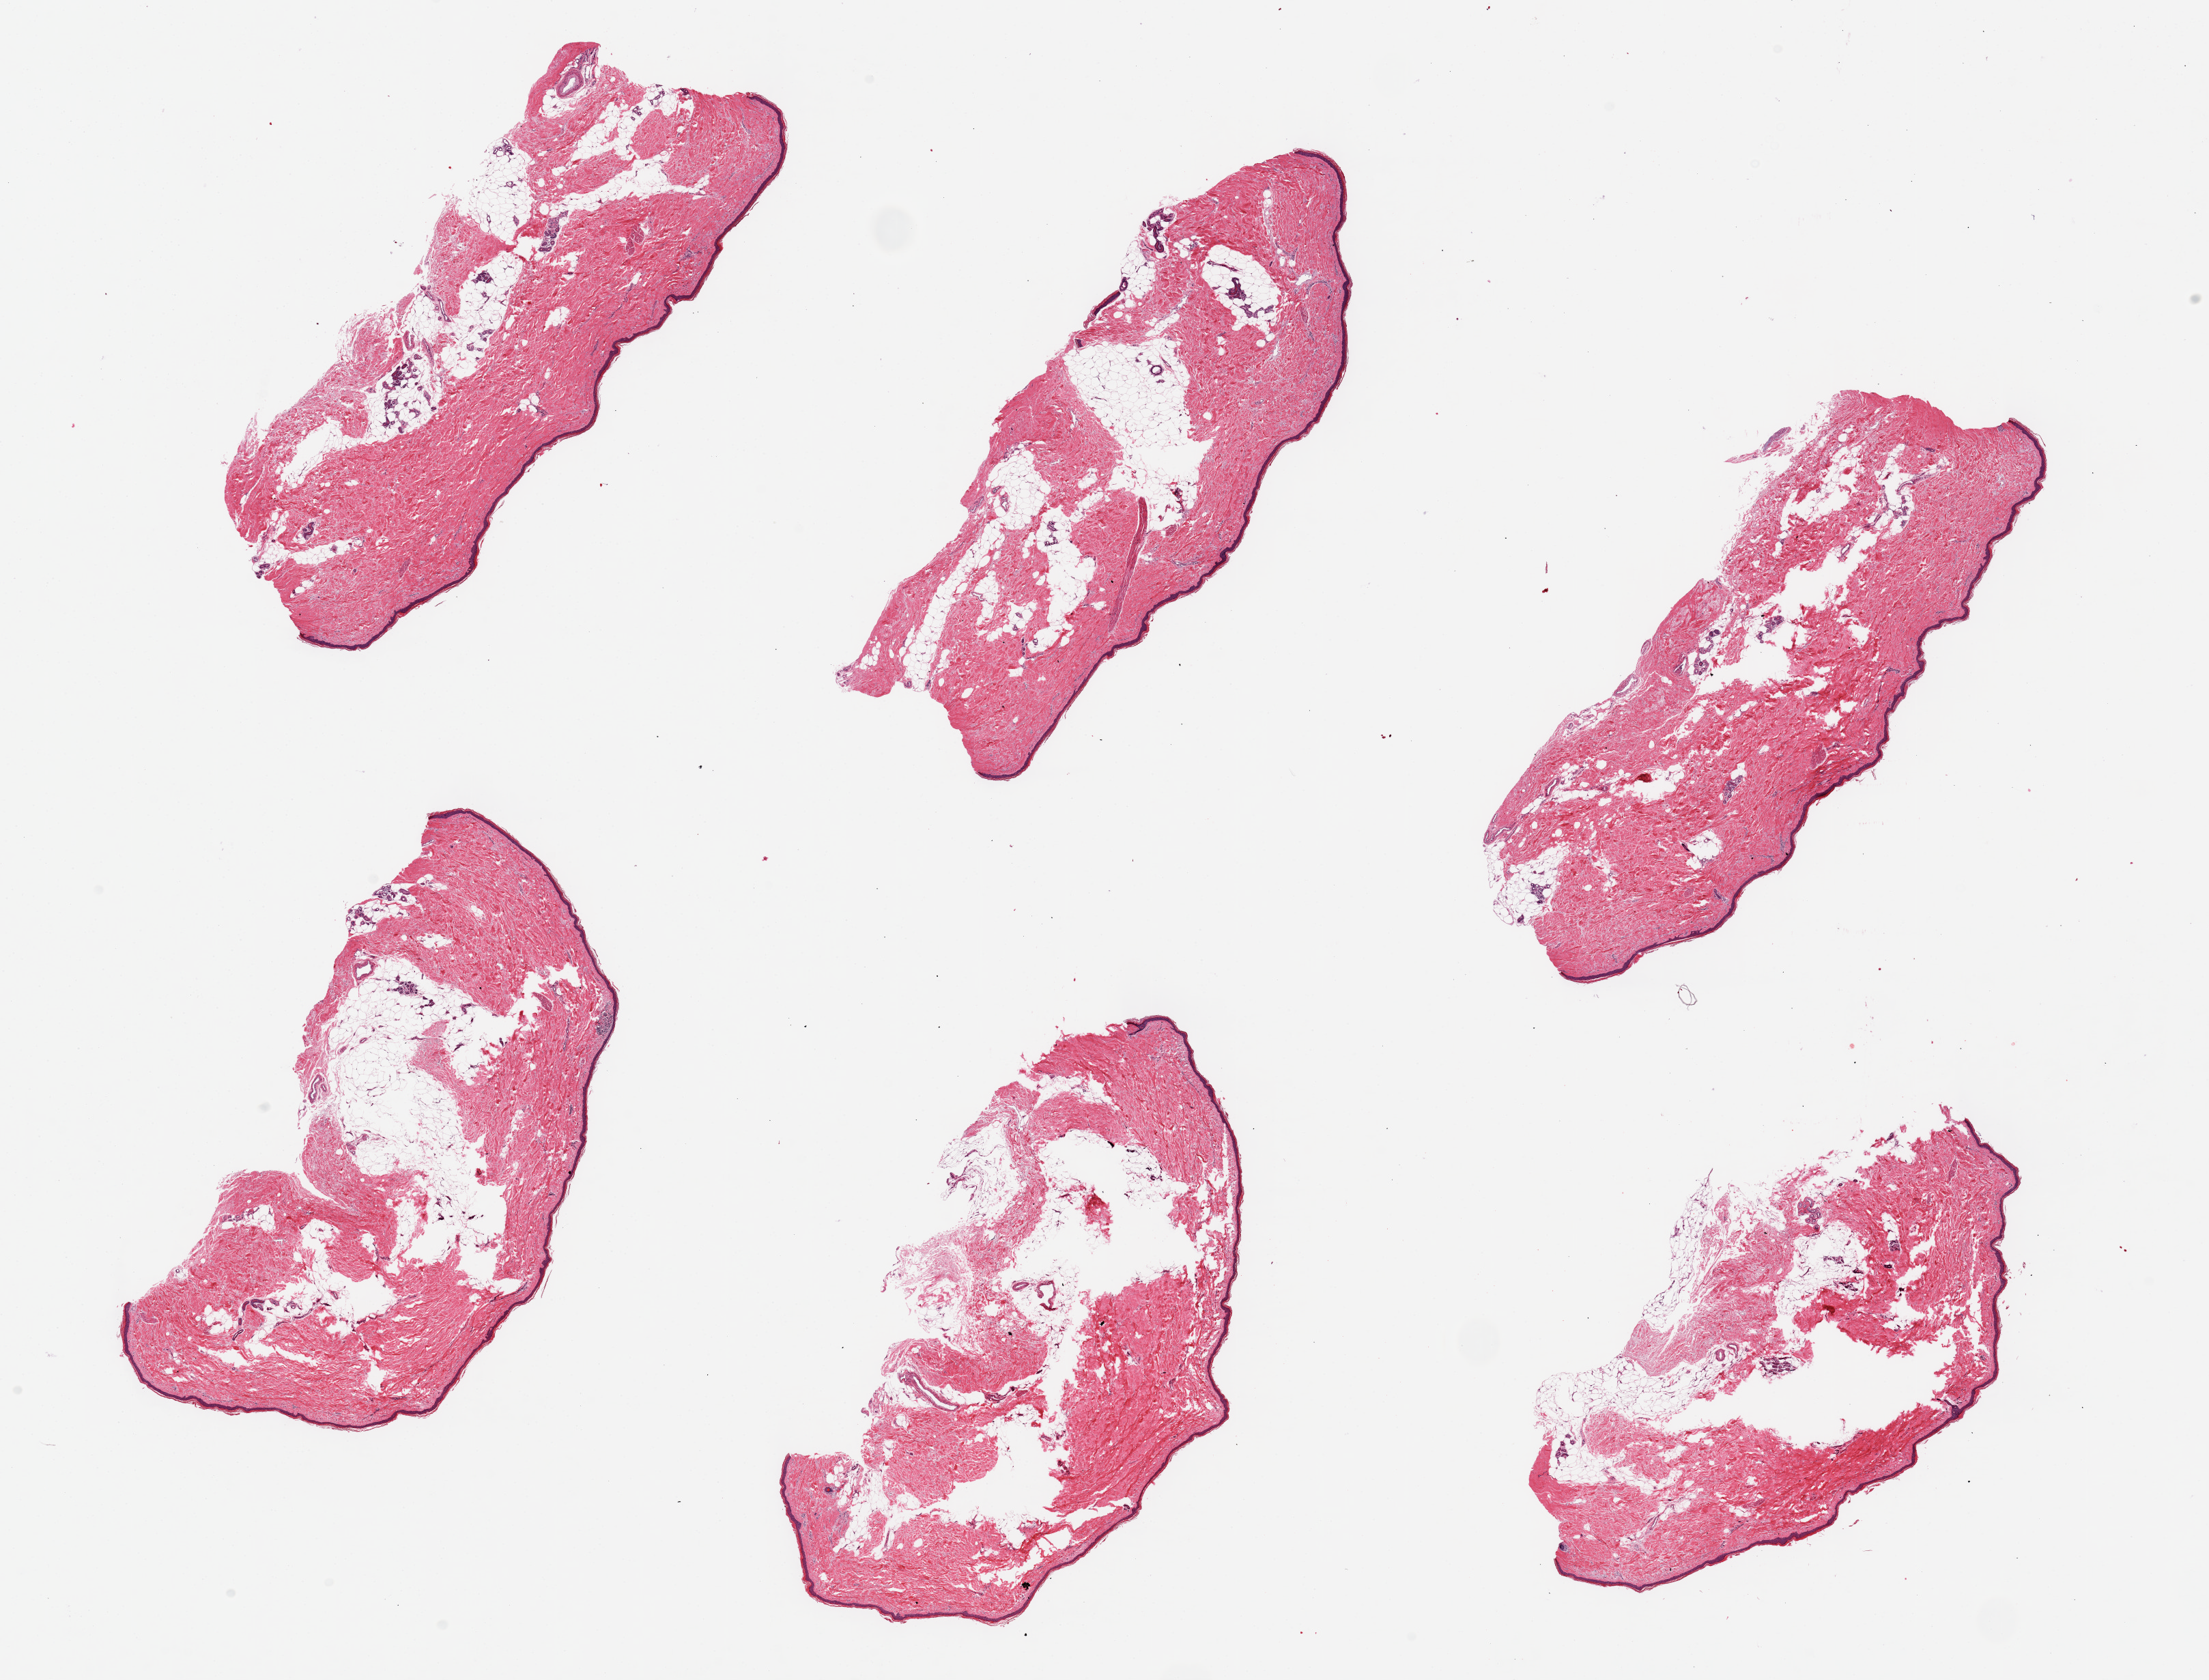
Whole-slide image, haematoxylin and eosin stain, low-resolution overview of the scanned area, about 25.6 x 19.5 mm (acquisition: 20x scan), PAXgene-fixed, paraffin-embedded tissue, sampled site (target tissue): skin of lower leg, tissue donor sample. Donor sex: female.
* reviewer comment on this tissue sample: 6 pieces ~7x3mm. Squamous epithelium is ~1-2% of thickness. ~20% of dermis contains intermingled fat, areas of extreme separation noted